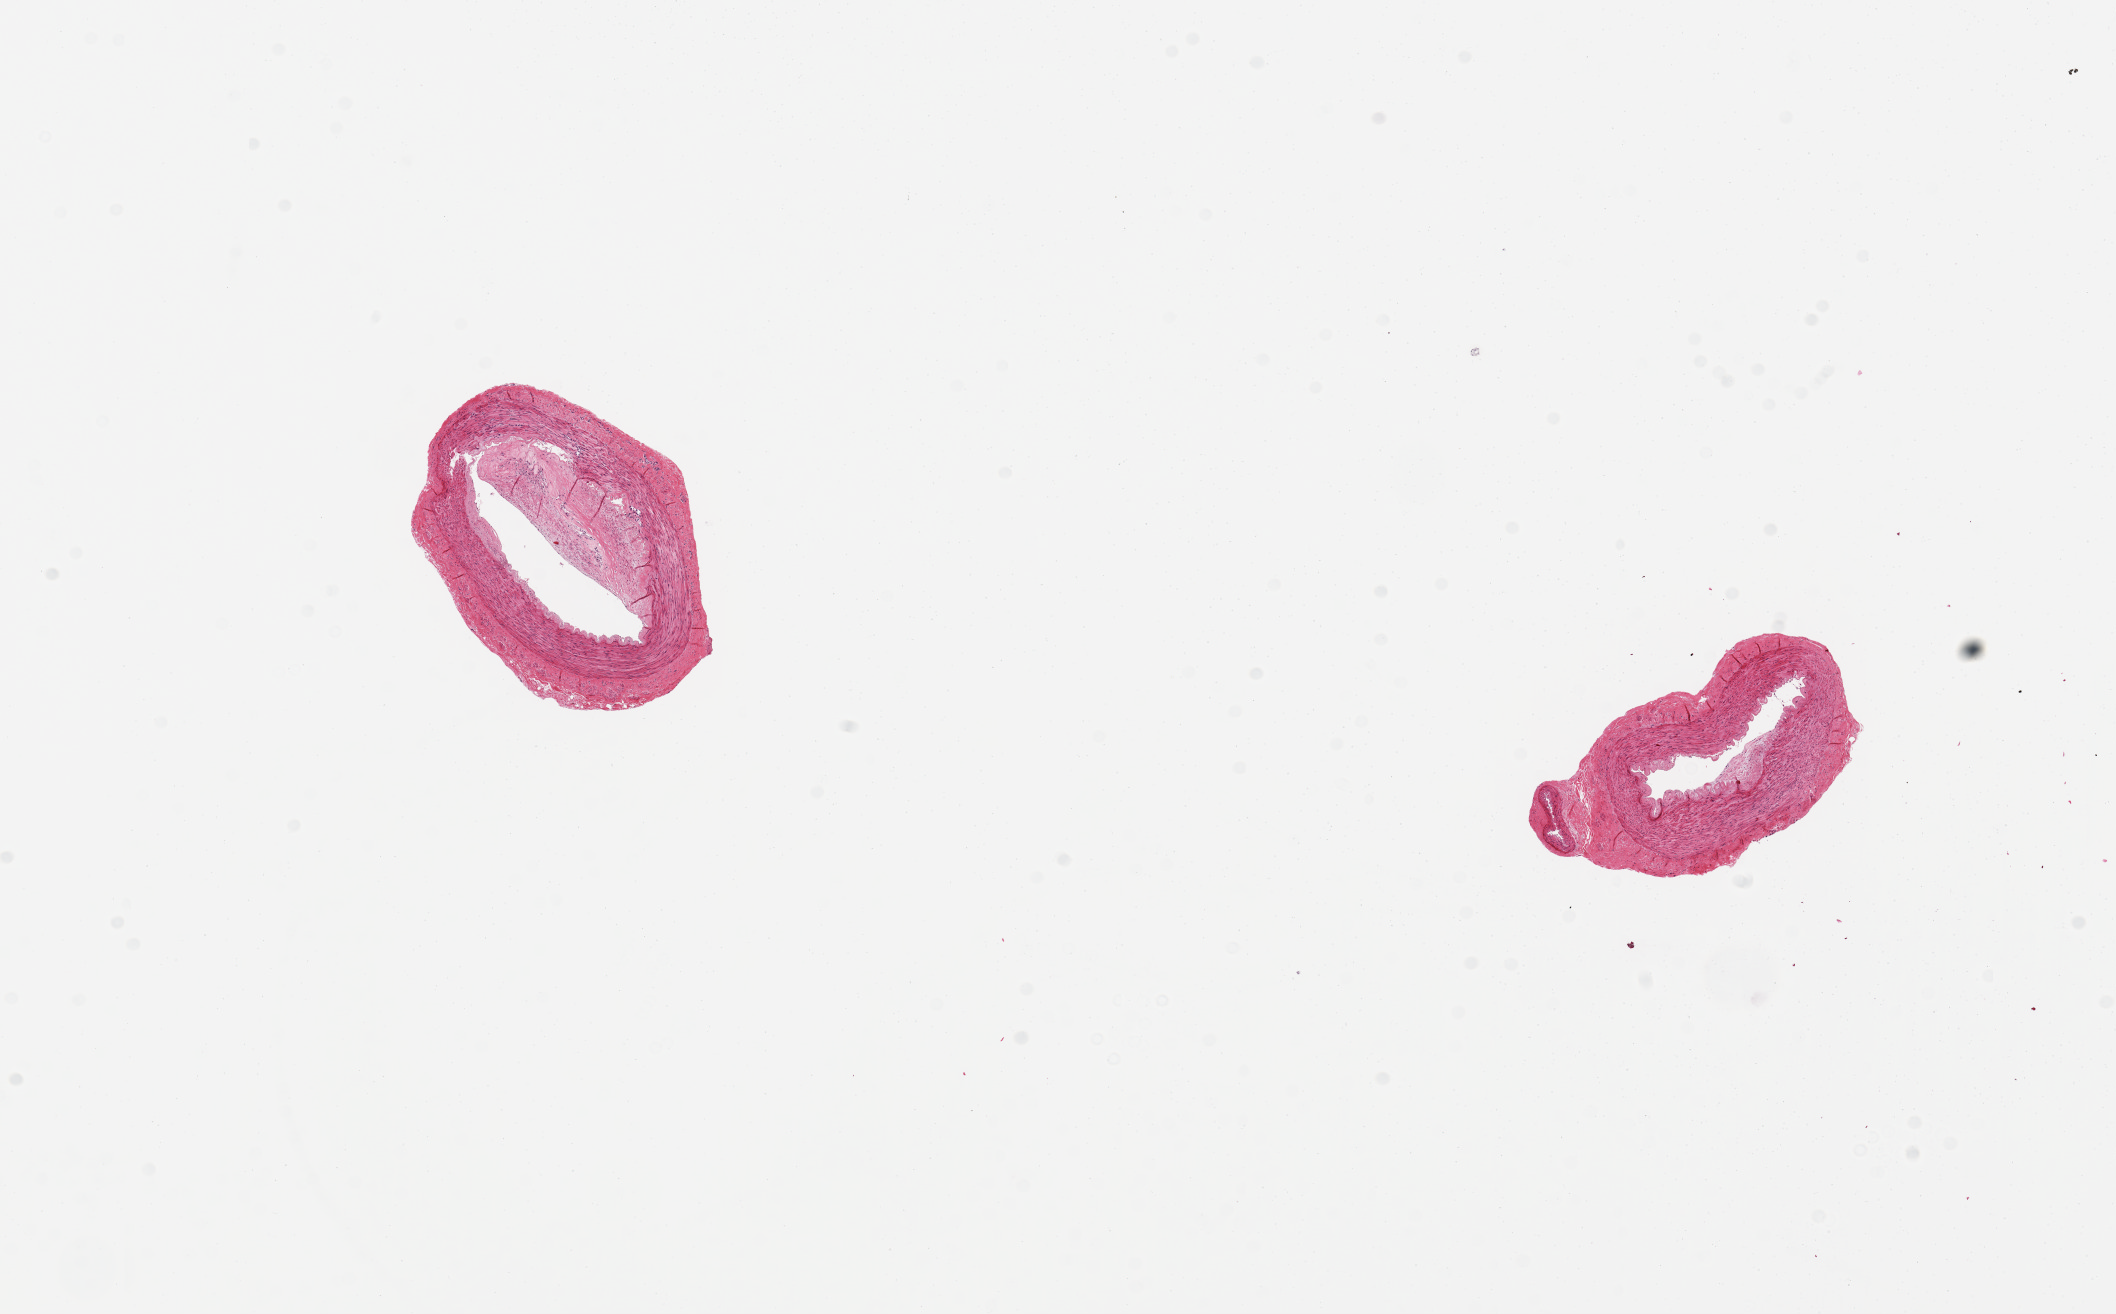
Whole-slide image, hematoxylin and eosin (H&E) stain — whole scanned area (about 16.7 x 10.4 mm) shown as a low-resolution overview. PAXgene-fixed, paraffin-embedded tissue. Sampled site (target tissue): tibial artery. Donor tissue sample. Donor sex: male.
Reviewer comment on this tissue sample: 2 pieces. 3x2 & 3x2mm; atherosclerotic occlusion ~60-70% of lumen.